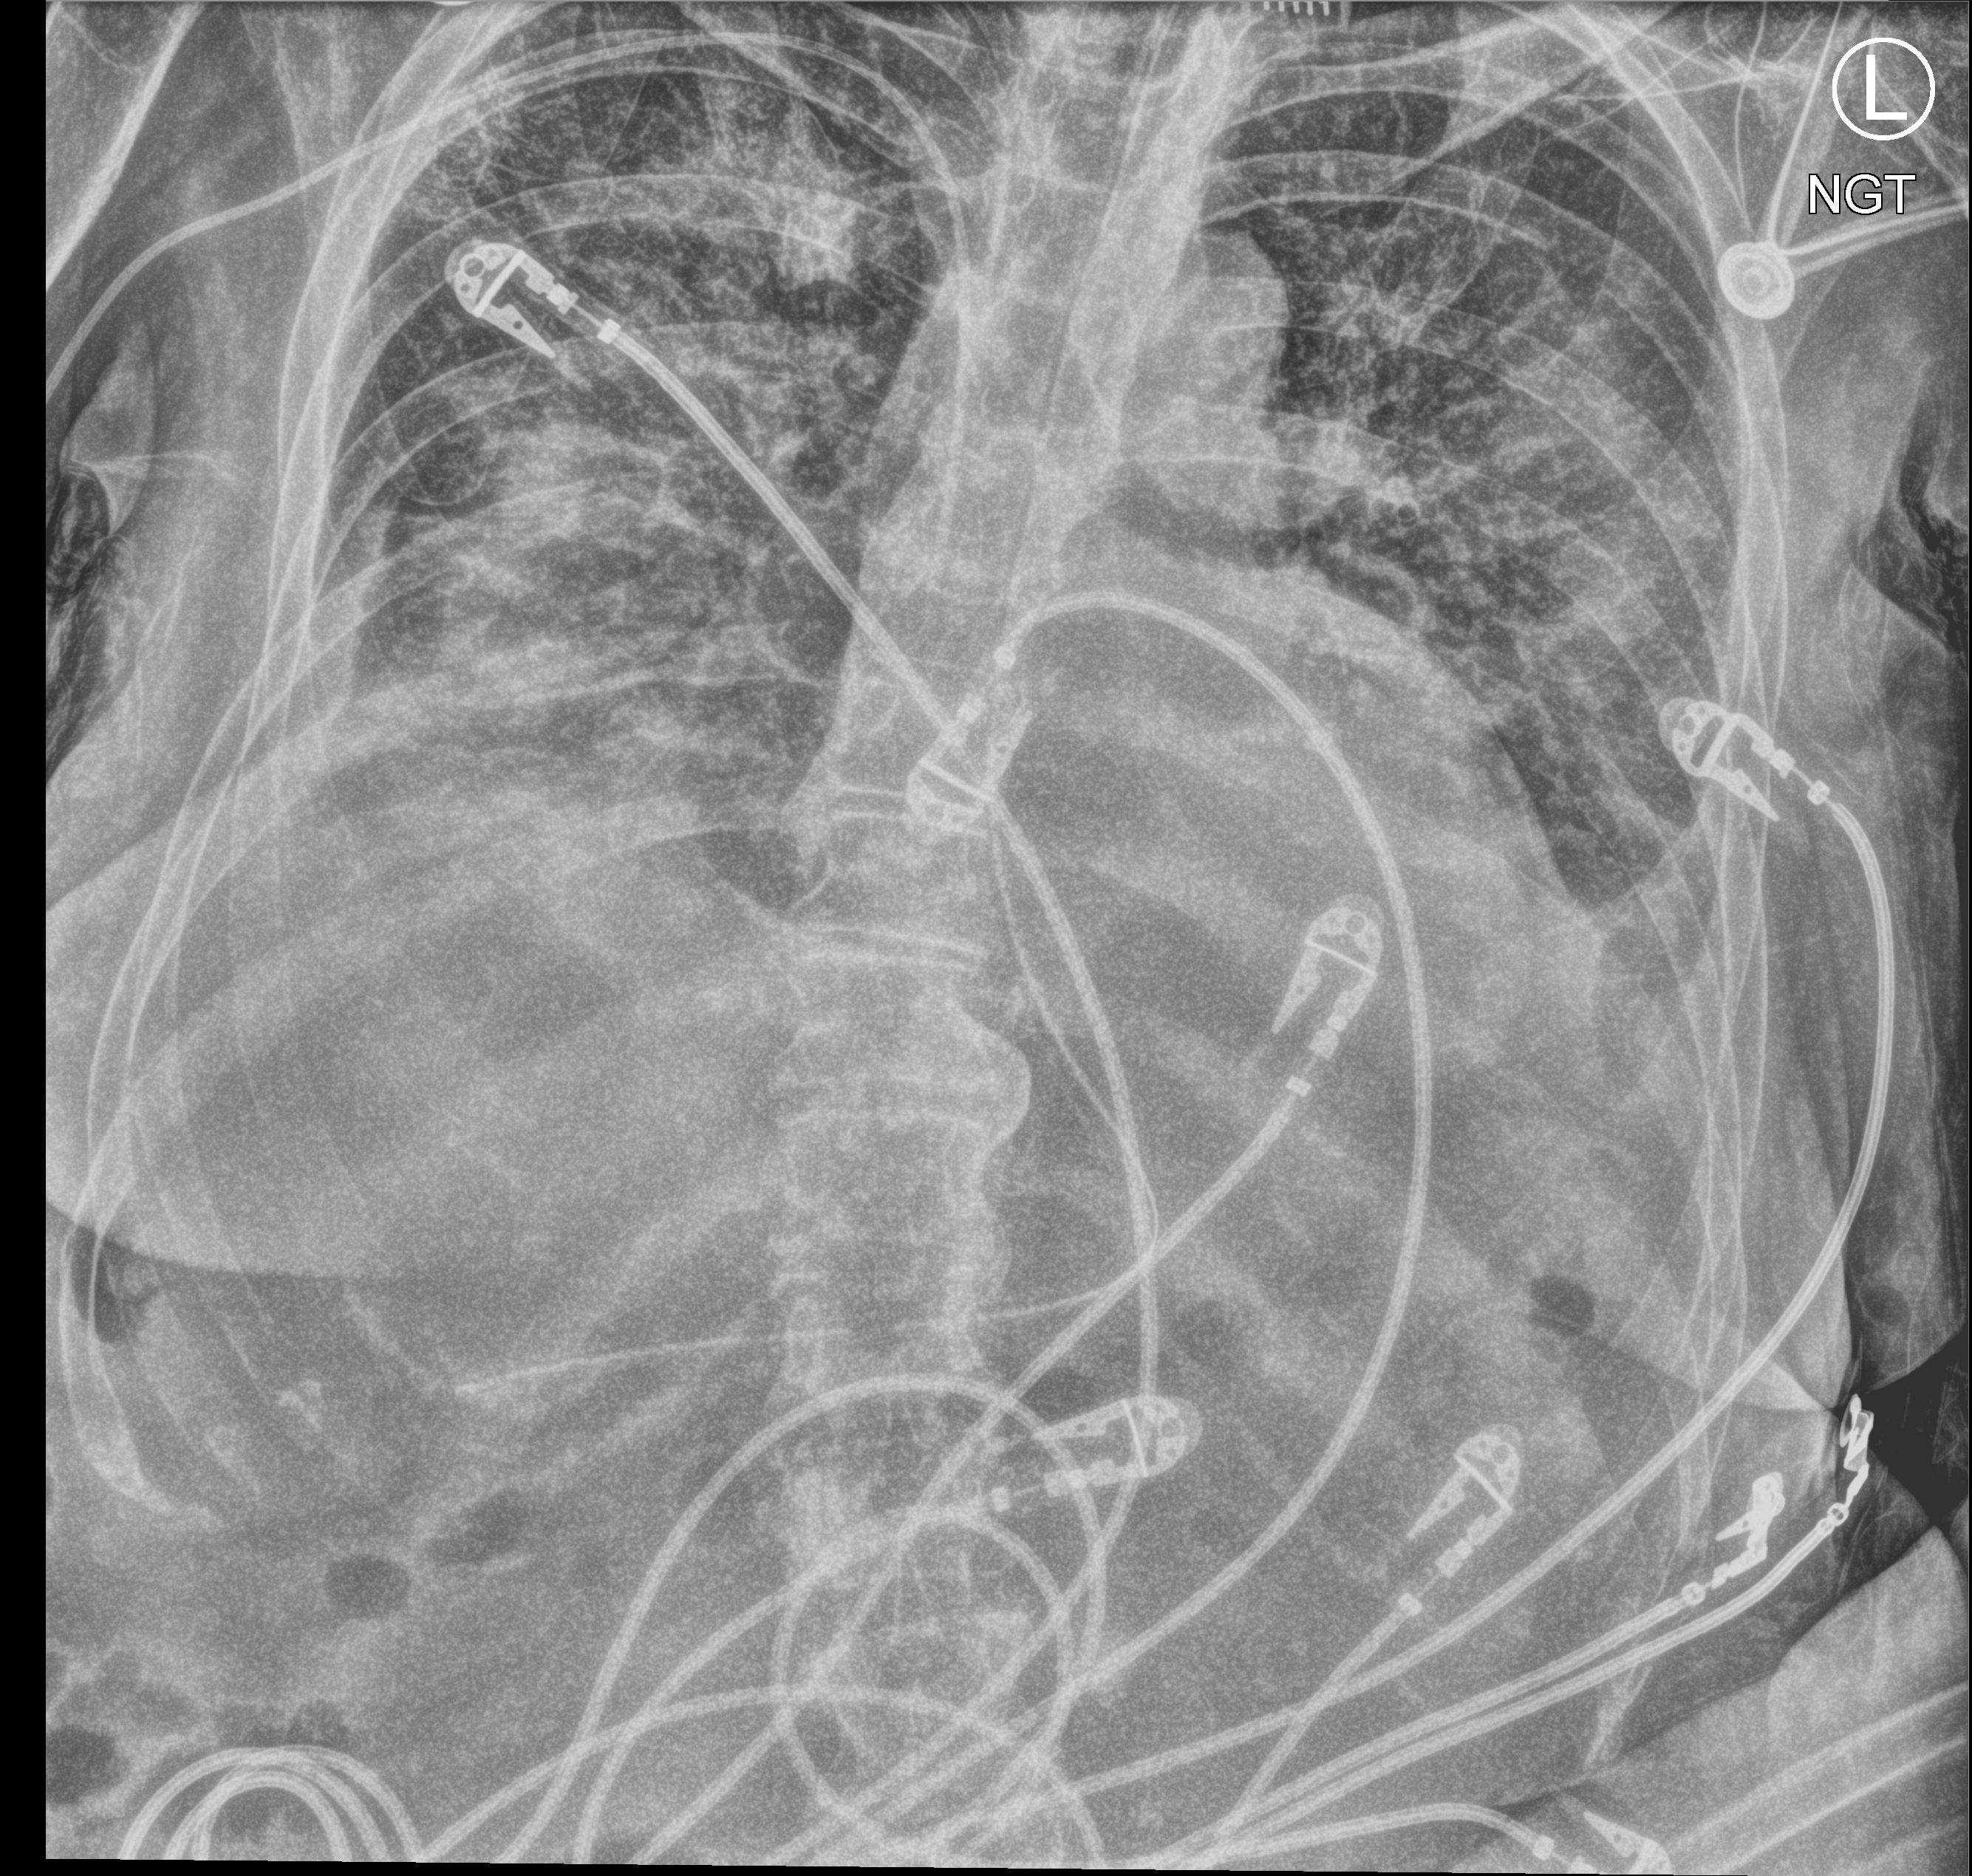
Bedside chest radiograph (computed radiography); anteroposterior (AP) projection. Patient hospitalised with COVID-19; female, aged 60–74 years.
Admission-level facts for this patient (not findings on this image; timing relative to this image not recorded):
- other chronic lung disease (admission record): no